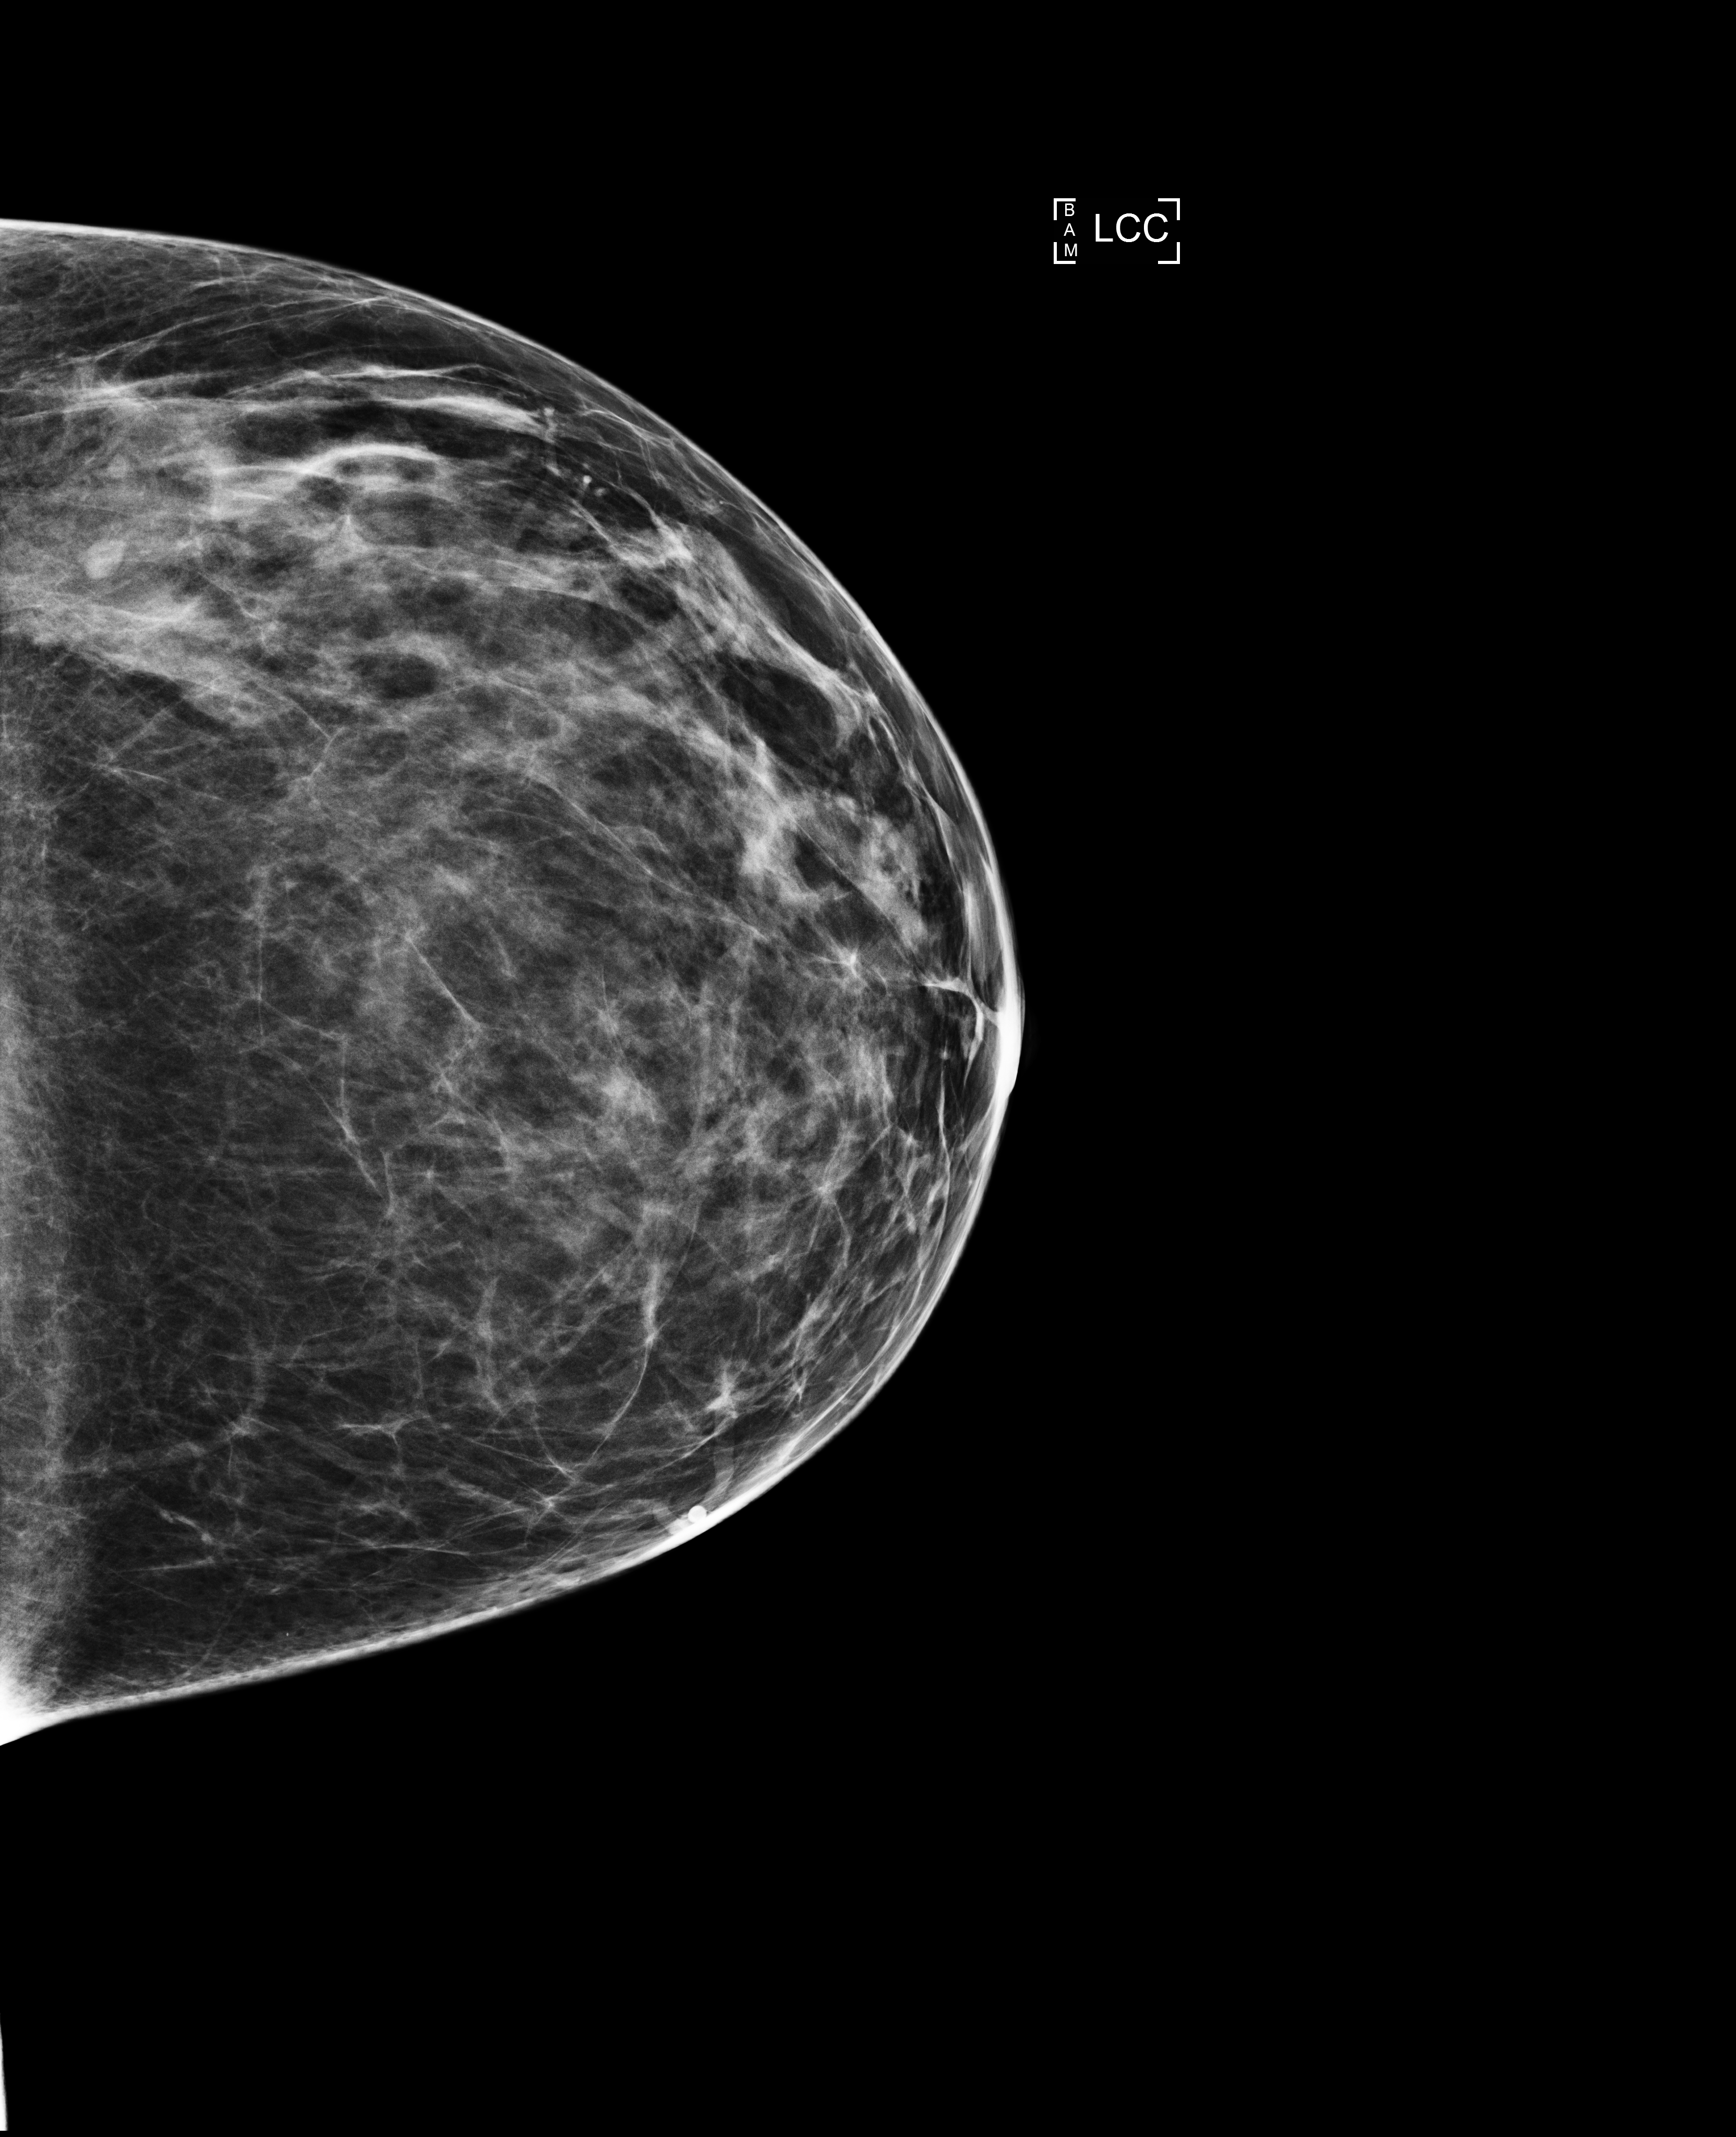
Annual screening mammography examination, system: Selenia Dimensions. Female patient, age 42 years.
Image type: full-field digital mammogram. Breast: left. Projection: CC view.